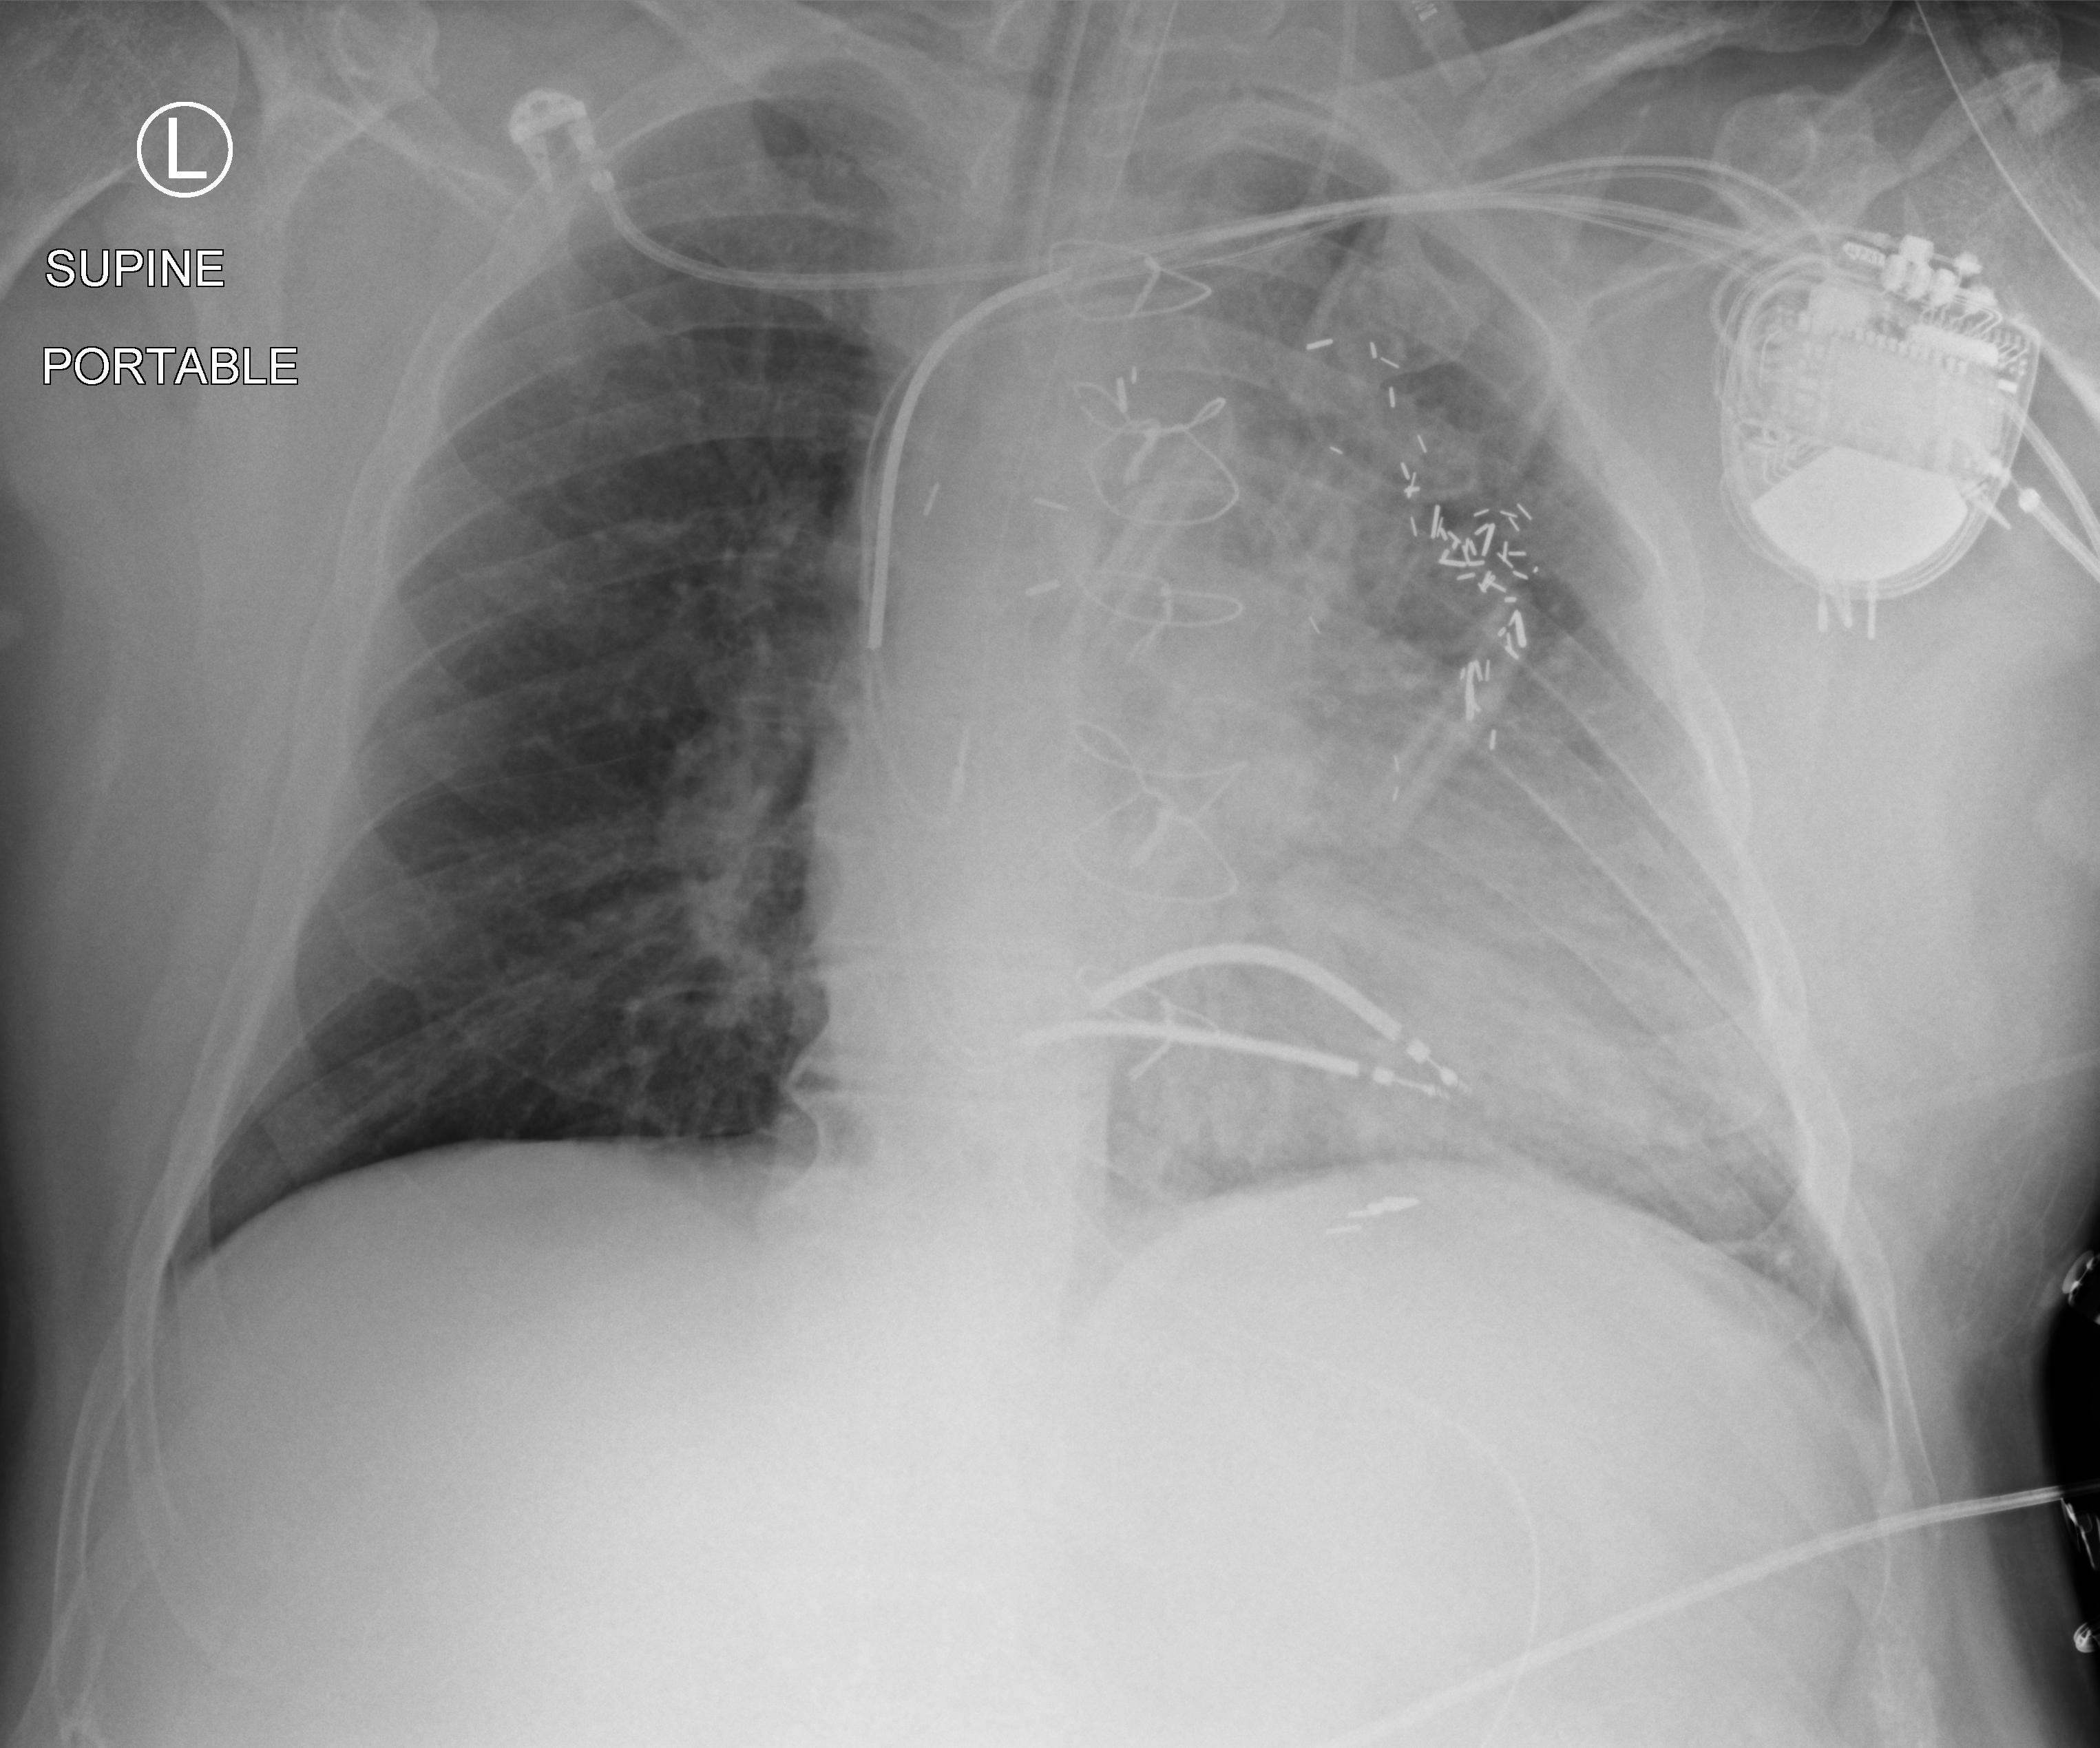
Portable chest radiograph, anteroposterior (AP) projection. Male patient hospitalised with COVID-19, age 60–74 years.
Admission-level facts for this patient (not findings on this image; timing relative to this image not recorded): length of hospital stay: 55 days; admitted to intensive care during this hospital stay: yes.